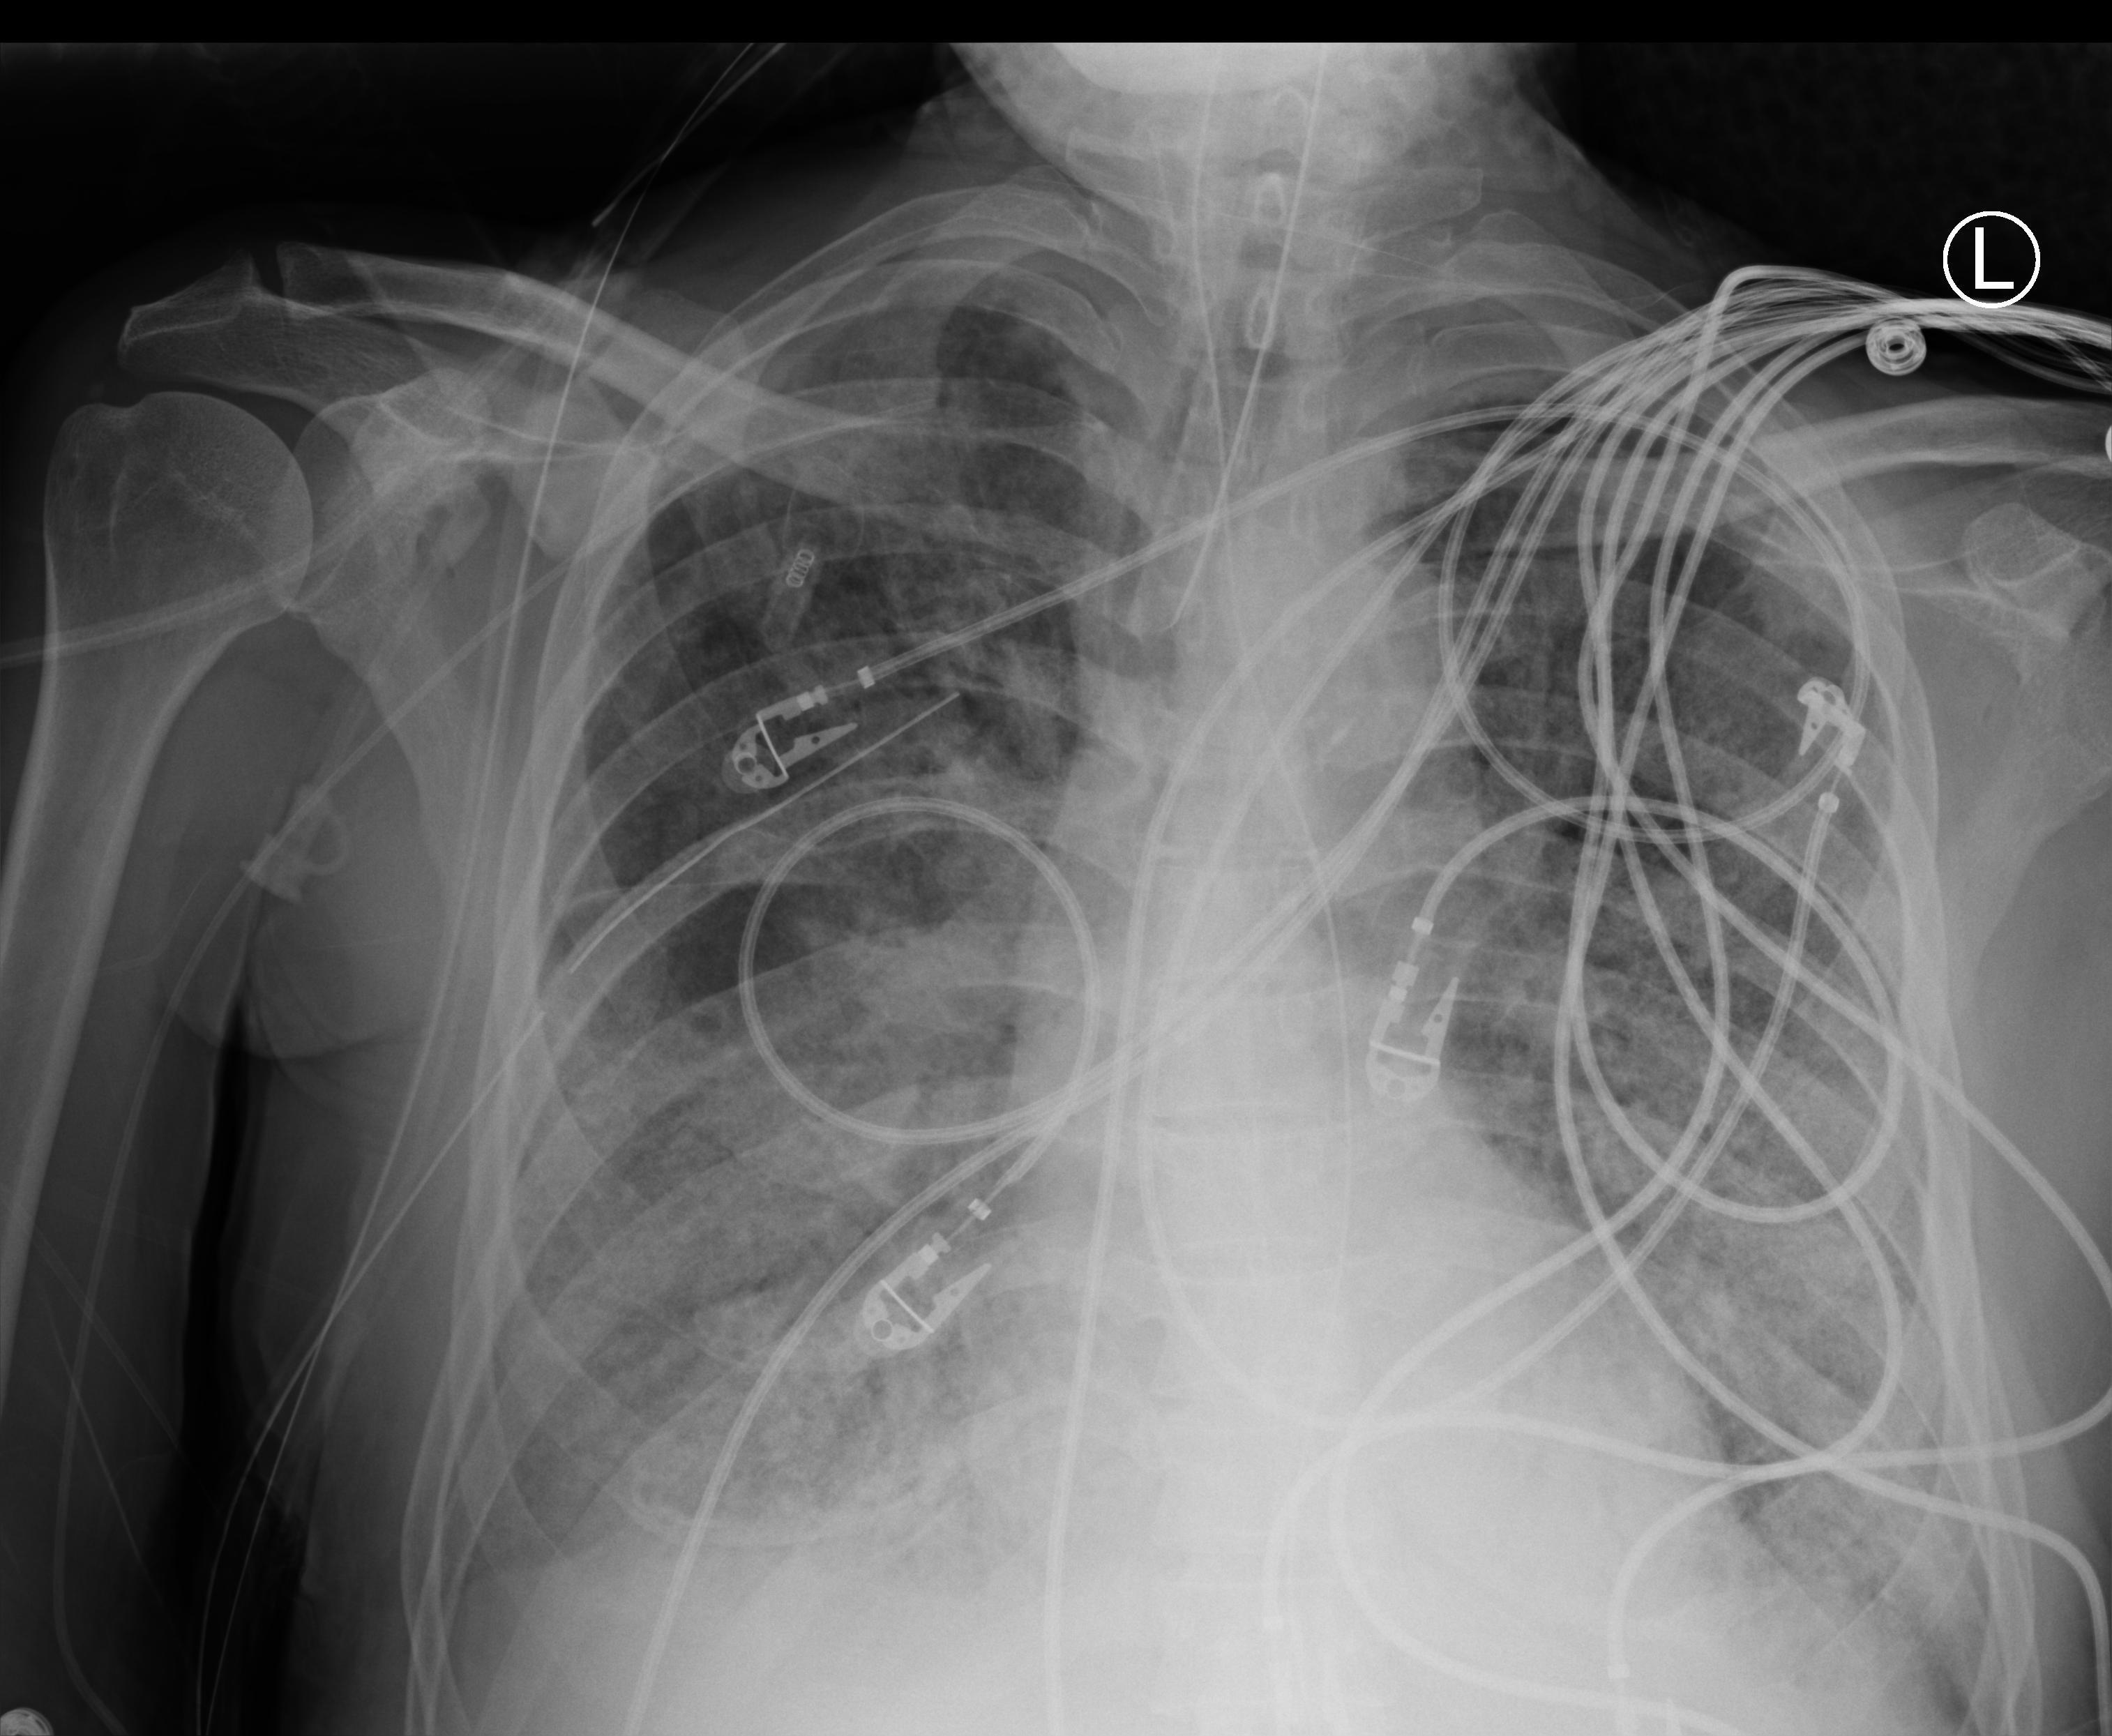
Chest X-ray (portable), anteroposterior (AP) projection. Male patient hospitalised with COVID-19, age 60–74 years.
From the hospital-stay record, not from the radiograph (when in the stay this image was taken is not recorded): diabetes (admission record): no; admitted to intensive care during this hospital stay: yes; mechanically ventilated during this hospital stay: yes.